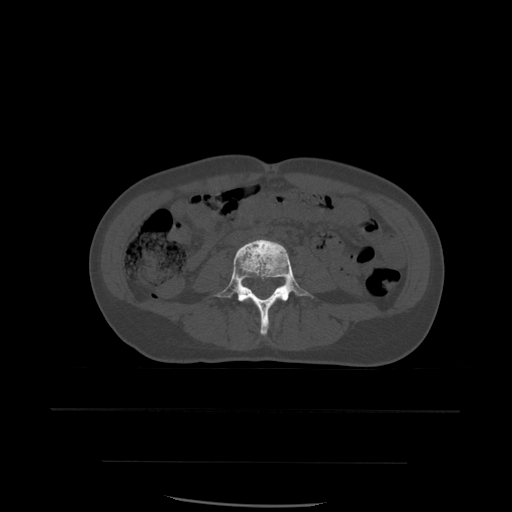
CT including the spine, one axial slice. Position 173 of 574 along the scan axis. Bone window (W 1800 / L 400 HU). 1.25 mm slice thickness. 512 × 512 image matrix. Patient age 48 years. Case-level facts recorded for this patient, not image findings: primary cancer: lung; vertebrae with lytic lesions (as recorded): T11.
Structures marked on this image (semi-automatic segmentation, software-assisted and operator-edited):
- L4 vertebra: box from (x=213, y=239) to (x=314, y=336) px